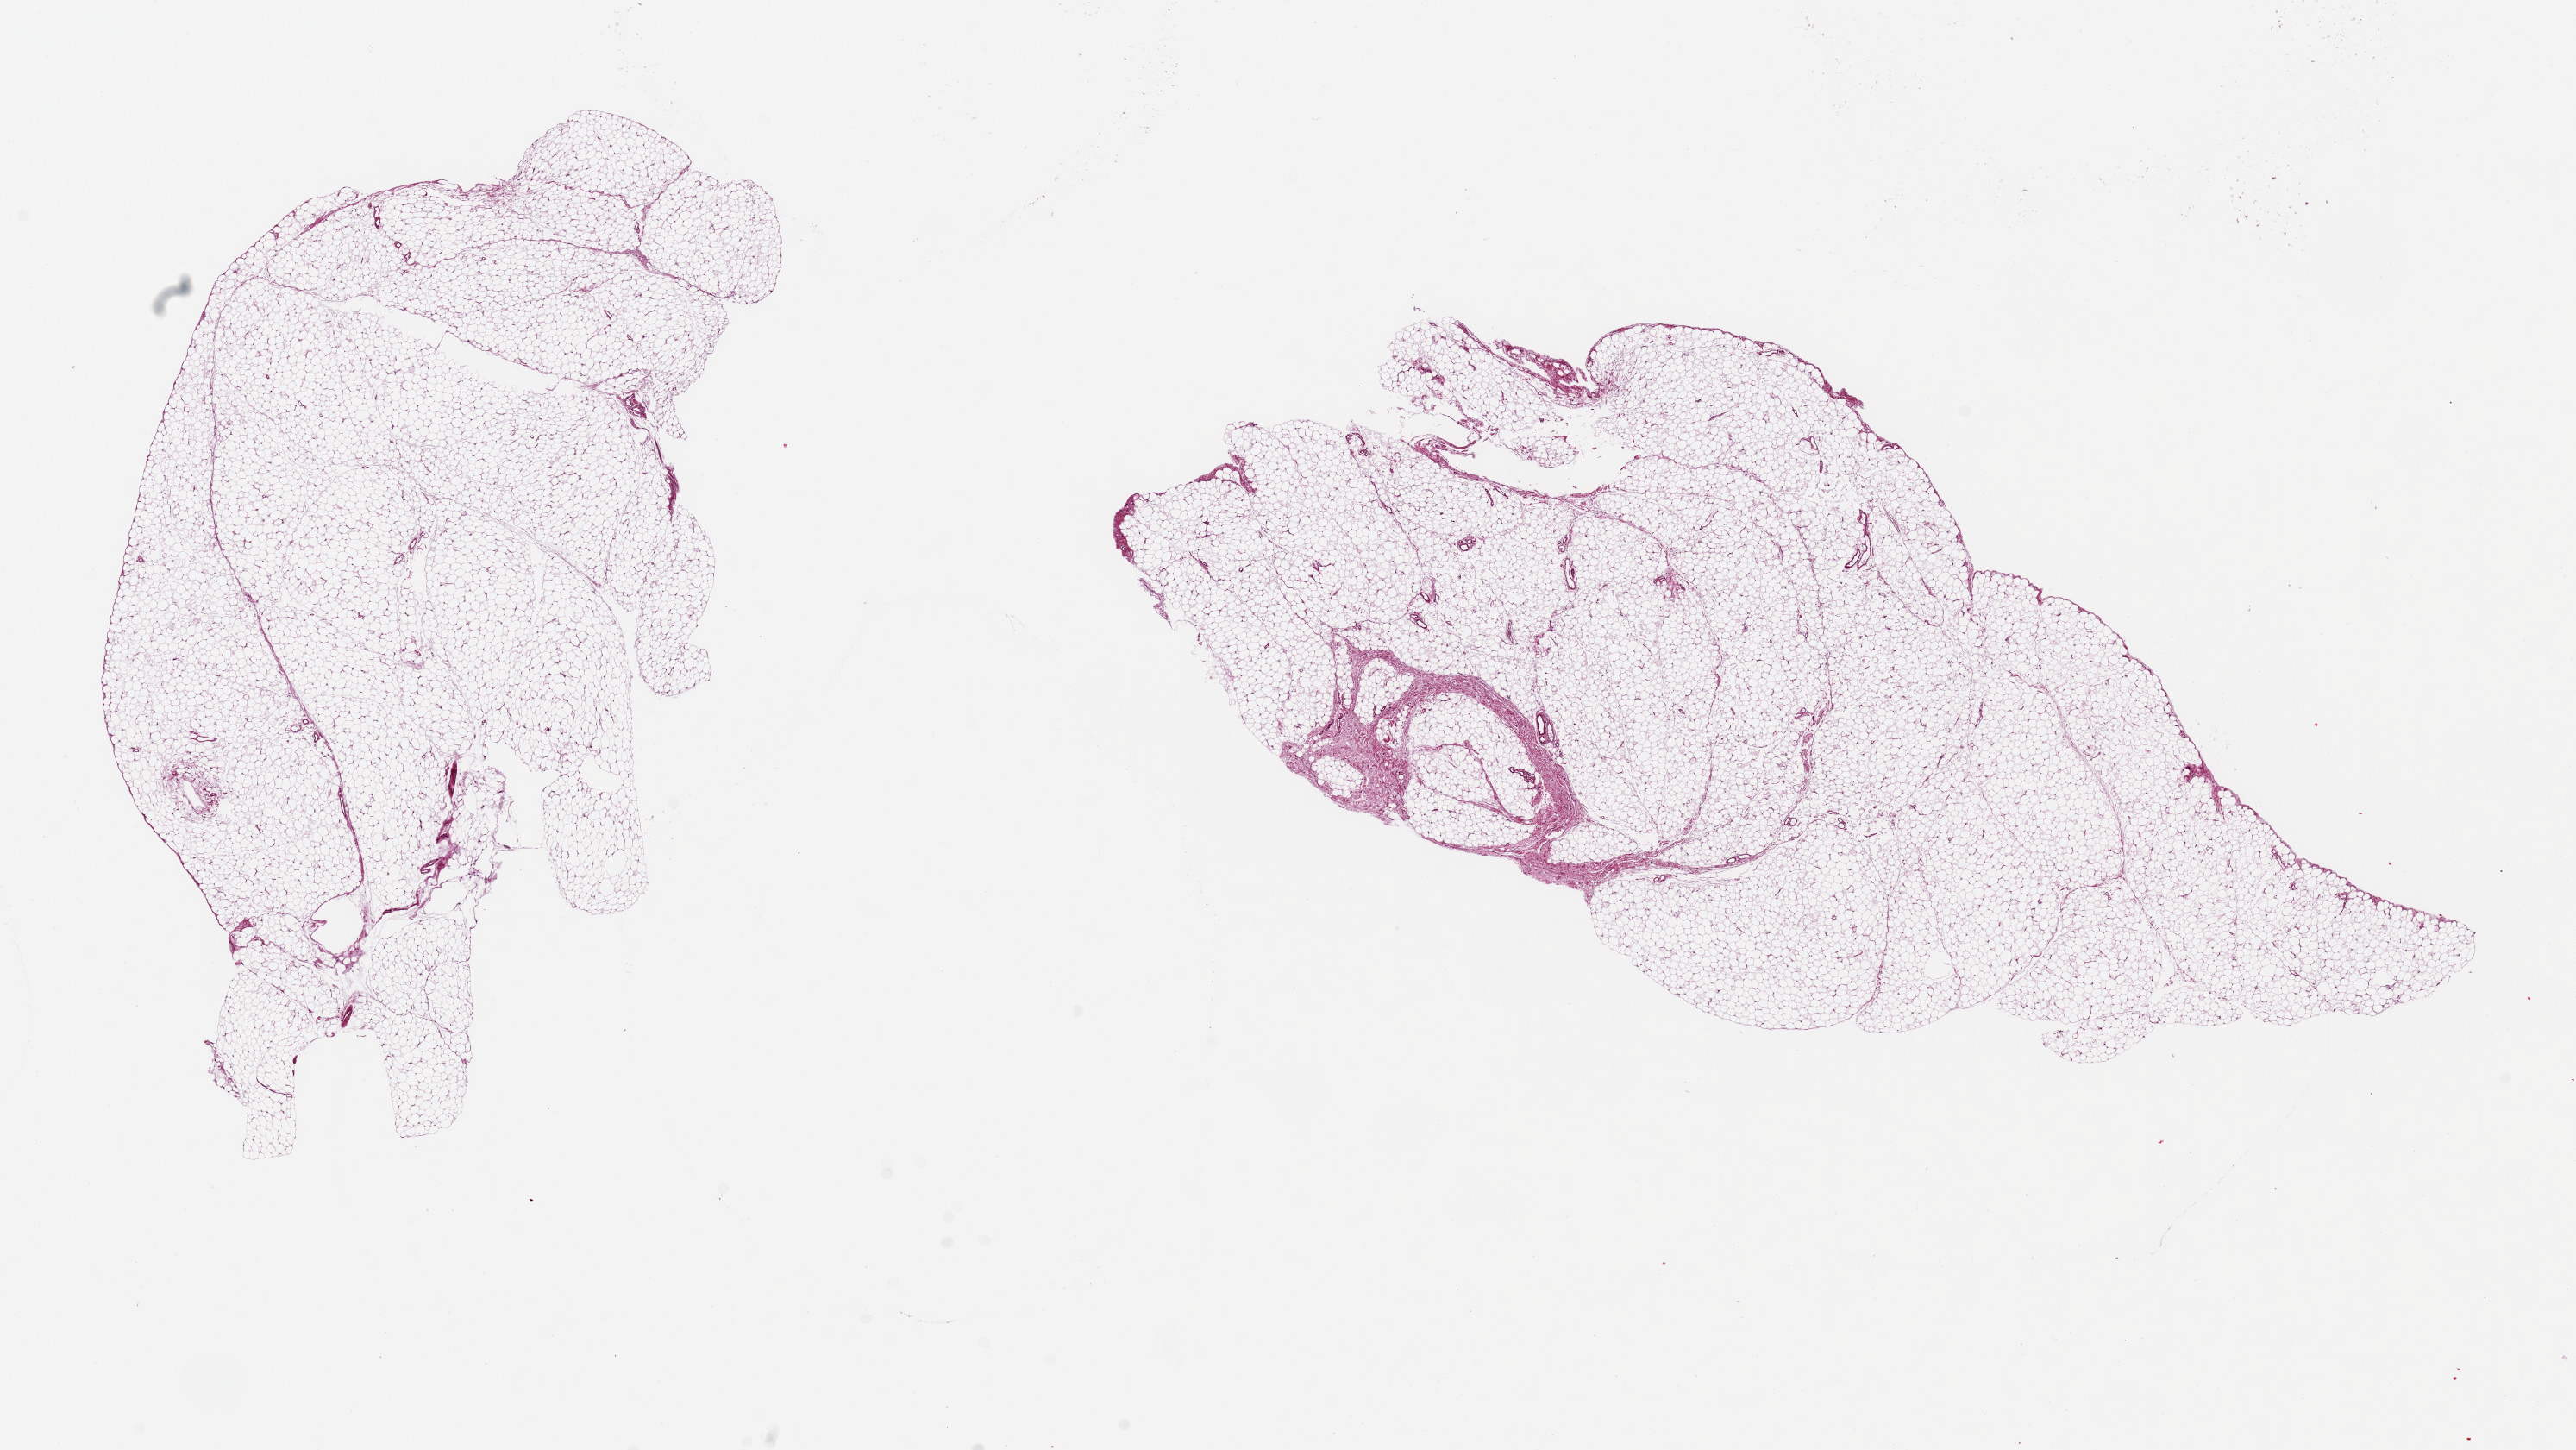
Whole-slide image, haematoxylin and eosin stain, brightfield — whole scanned area (about 23.6 x 13.3 mm) shown as a low-resolution overview, PAXgene-fixed, paraffin-embedded tissue, section of omentum (target tissue), donor tissue sample. Female donor.
Pathologist's review note for this sample: 2 pieces, 13x6 & 10x5.5mm.